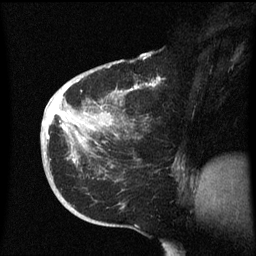
Breast MRI (dynamic contrast-enhanced), one sagittal slice. Slice 28 of 60 in the series (ordered by position). Dynamic contrast-enhanced series, image 2 of 3 at this slice position (ordered by acquisition). 1.5 T. TE 4.2 ms, TR 8.4 ms. 2.3 mm slice thickness. 256 × 256 image matrix. Female patient, age 38 years. Case-level facts recorded for this patient, not image findings: setting: breast cancer imaged before/during neoadjuvant chemotherapy; receptor status: HER2-positive.
Annotated regions visible in this slice (semi-automatic segmentation, software-assisted and operator-edited):
- analysis volume of interest (the breast-tissue region the enhancement analysis was run in; not a lesion): bounding box <41,78,187,213> (left, top, right, bottom; pixels)
- tumour enhancement mask (voxels above the 70 % enhancement threshold inside the analysis volume of interest): <47,84,154,163>